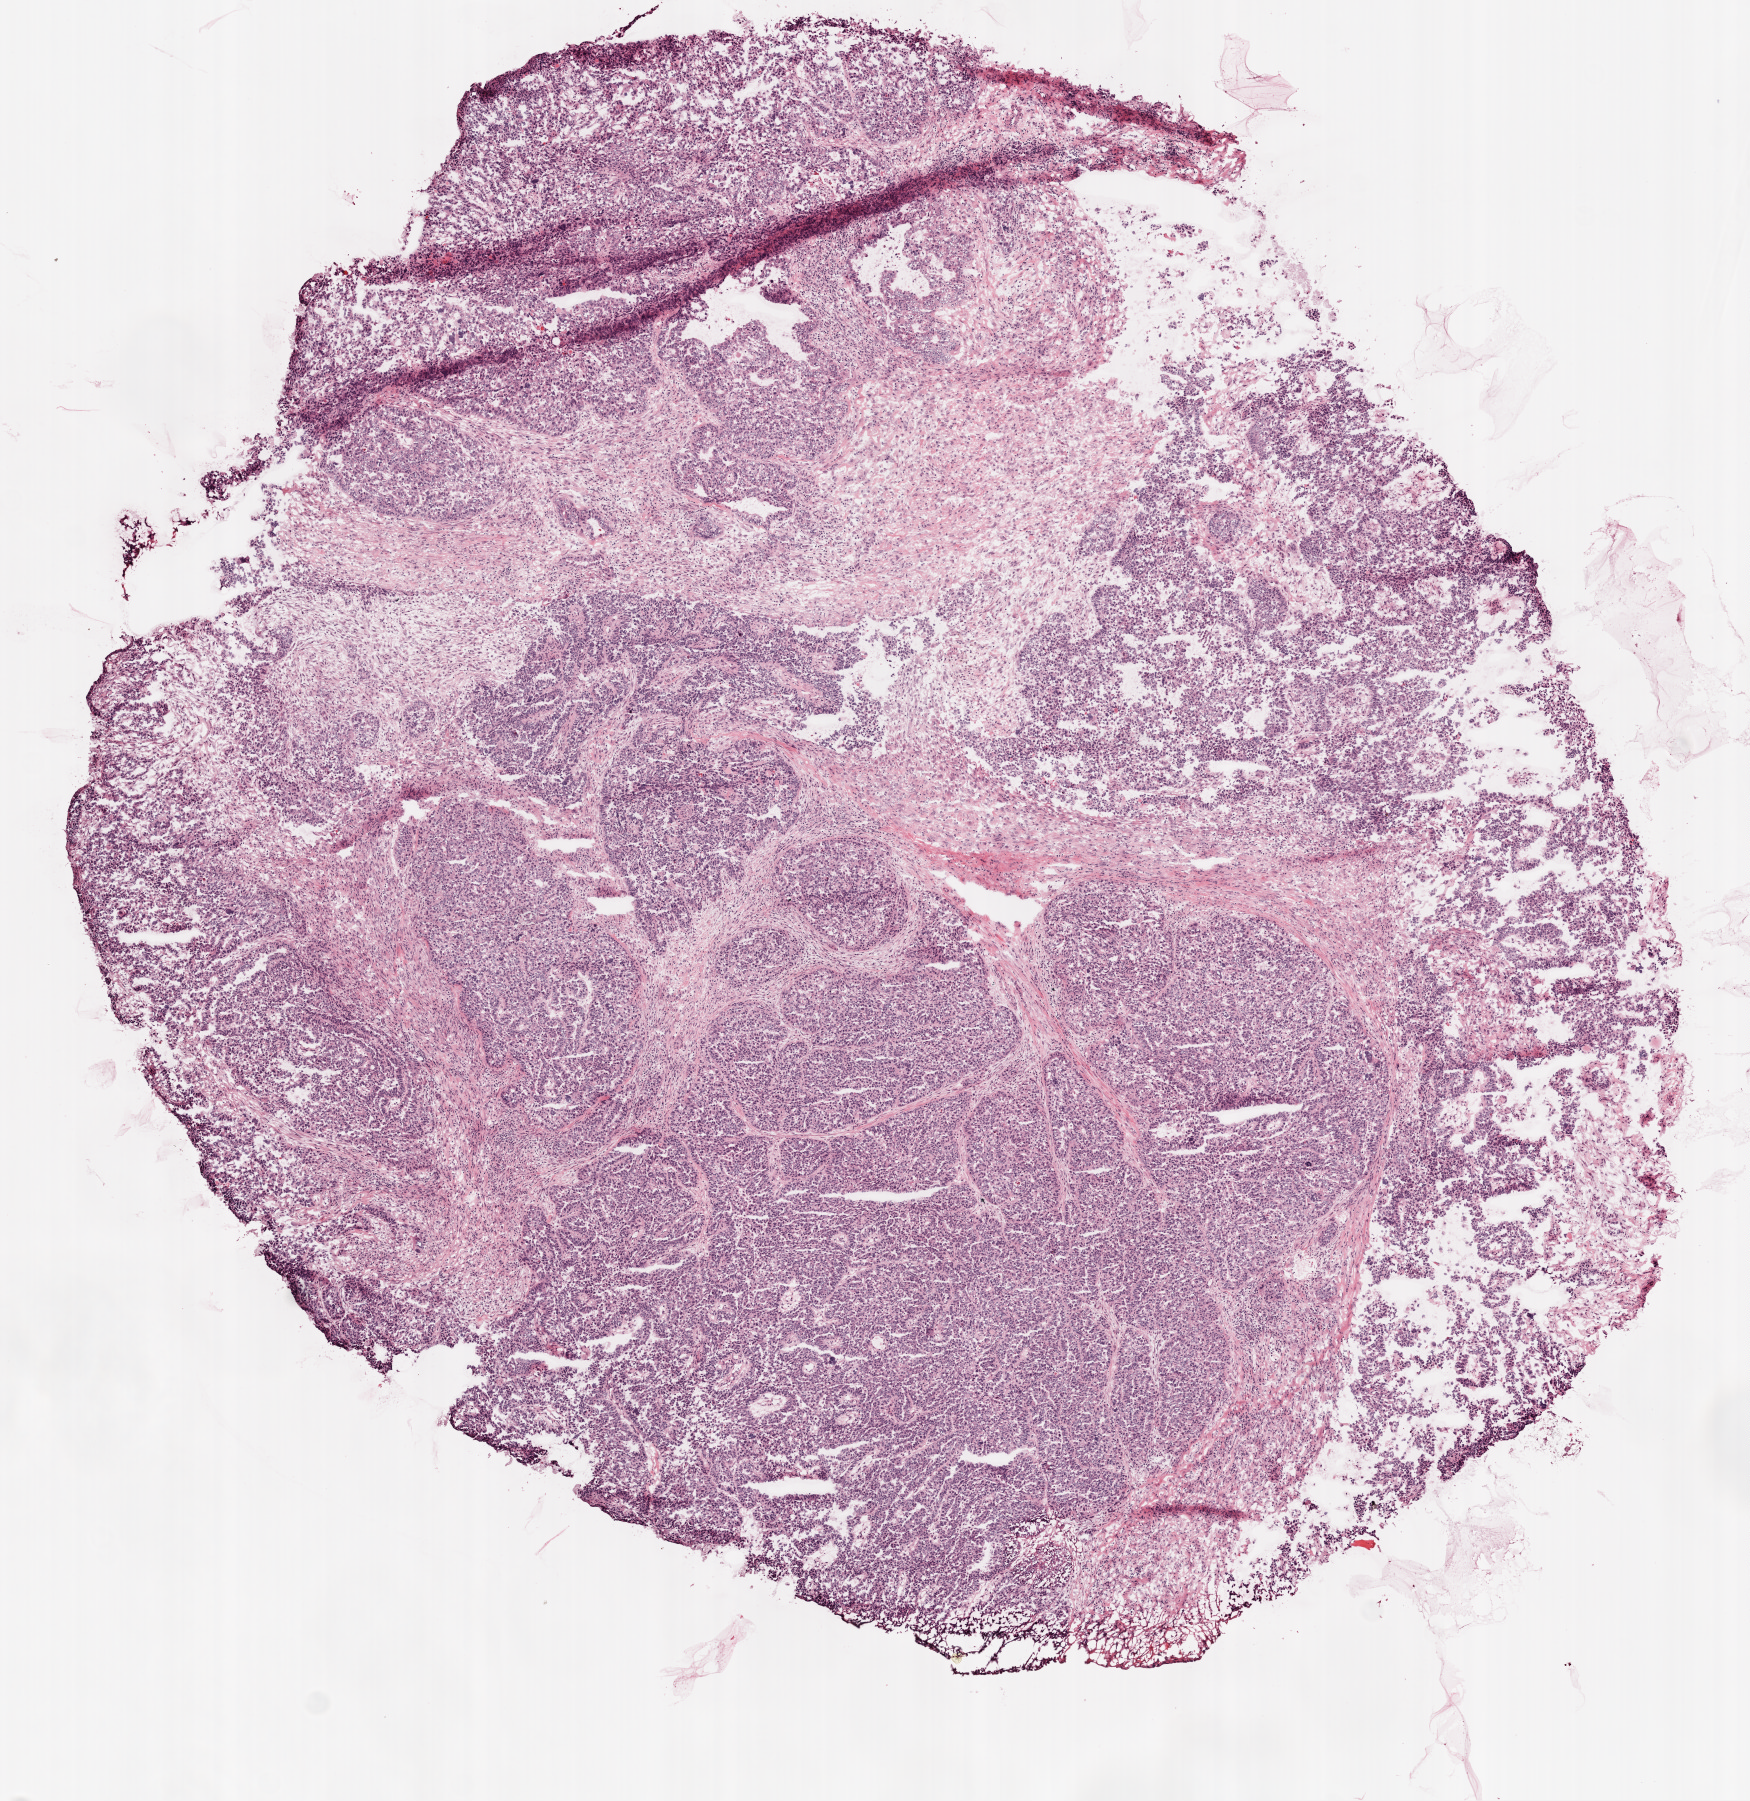
Digitized Hematoxylin and eosin (H&E) stained tissue section (whole slide) — whole scanned area (about 7.0 x 7.2 mm, slide scanned at 20x) shown as a low-resolution overview. Frozen section. Ovary, primary tumour sample. Patient: female, age at initial diagnosis 51 years. Histologic grade: G2 (moderately differentiated). Slide review estimates, as recorded: tumour cells 98%, tumour nuclei 90%, normal cells 0%, stromal cells 0%, necrosis 2%. Inflammatory infiltration, as recorded: monocyte infiltration 1%.
Laterality: bilateral. FIGO stage: IIIC. Histologic diagnosis: Serous cystadenocarcinoma, NOS.